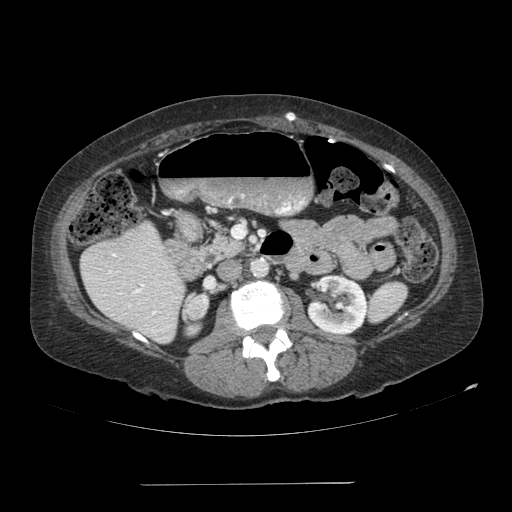
Contrast-enhanced abdominal CT, one axial slice; slice 46 of 113 in the series (ordered by position); 120 kVp; soft-tissue window (W 400 / L 40 HU); 2.5 mm slice thickness; 512 × 512 image matrix, field of view 440 × 440 mm. Female patient, age 67 years. From the clinical record (not read from this slice): diagnosis: adrenocortical carcinoma; tumour side: right adrenal; tumour size at pathology: 9.8 cm; Ki-67 index: 59 %; stage (as recorded): 4.
Annotated regions visible in this slice (semi-automatic segmentation, software-assisted and operator-edited):
- mass: box from (x=187, y=294) to (x=207, y=318) px